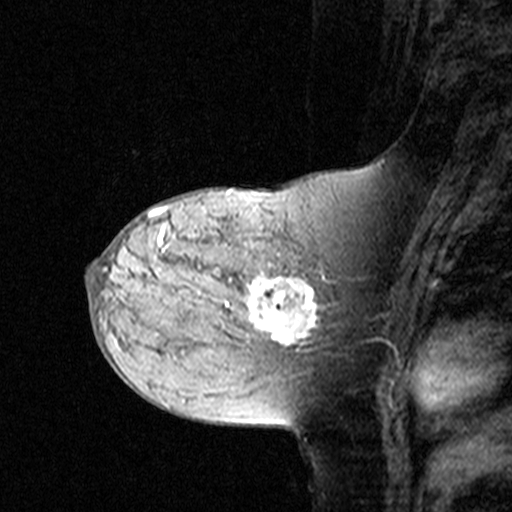
Breast MRI (dynamic contrast-enhanced), one sagittal slice; position 17 of 44 along the scan axis; dynamic contrast-enhanced study with each time point stored as its own series, time point 2 of 3 at this slice position (early post-contrast, ordered by acquisition time); 1.5 T; TE 4.5 ms, TR 11 ms; 3 mm slice thickness; 512 × 512 image matrix, field of view 200 × 200 mm. Patient: female, 44 years. Case-level facts recorded for this patient, not image findings: setting: breast cancer imaged before/during neoadjuvant chemotherapy; receptor status: triple-negative.
Annotated regions visible in this slice (semi-automatically segmented with operator editing):
- analysis volume of interest (the breast-tissue region the enhancement analysis was run in; not a lesion): bounding box <142,208,349,363> (left, top, right, bottom; pixels)
- tumour enhancement mask (voxels above the 90 % enhancement threshold inside the analysis volume of interest): <147,210,318,346>